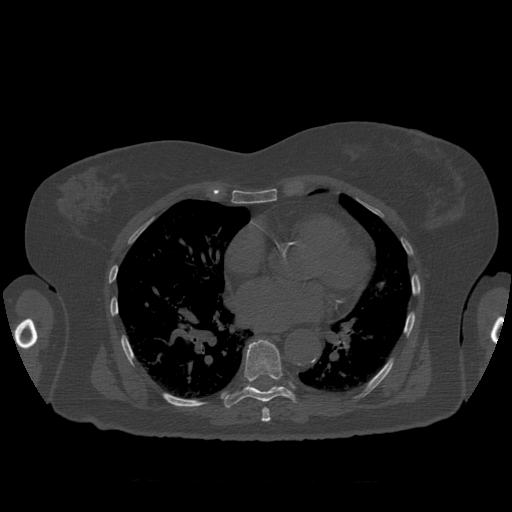
CT including the spine, one axial slice; slice 378 of 399 in the series (ordered by position); 120 kVp; bone window (W 1800 / L 400 HU); 1.25 mm slice thickness; 512 × 512 image matrix, field of view 404 × 404 mm. Patient age 81 years. From the clinical record (not read from this slice): primary cancer: renal; vertebrae with lytic lesions (as recorded): L1.
Annotated regions visible in this slice (semi-automatic segmentation, software-assisted and operator-edited):
- T7 vertebra: box from (x=262, y=407) to (x=271, y=422) px
- T8 vertebra: (x=223, y=340)–(x=297, y=408)